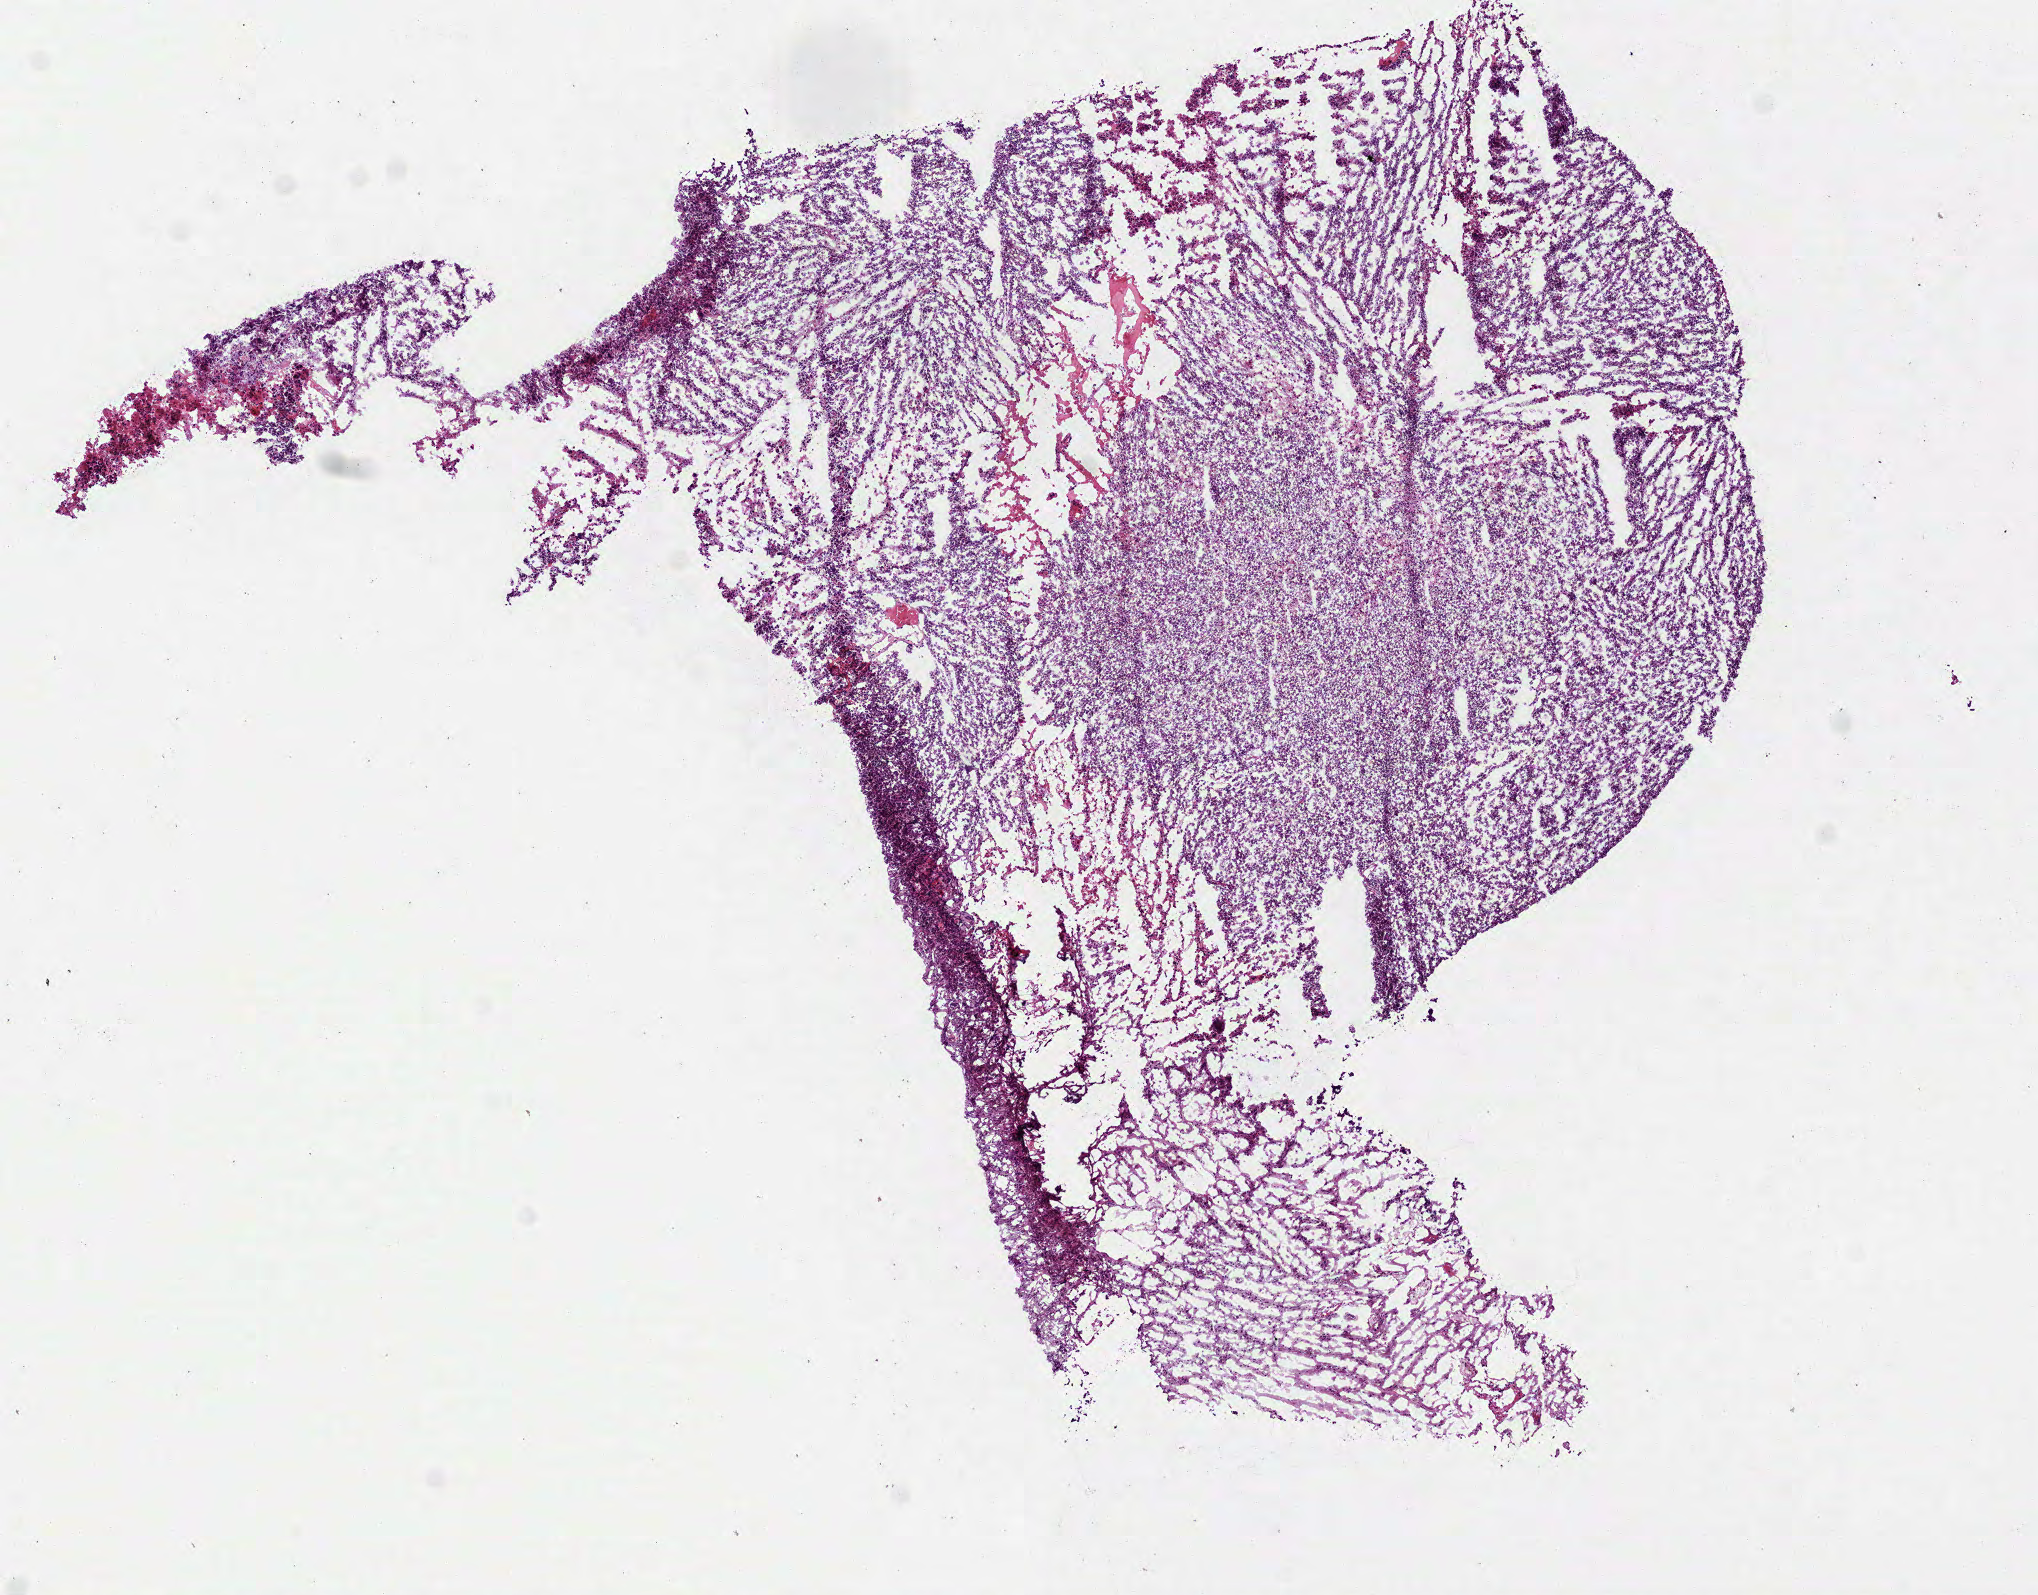
Whole-slide histology image, H&E, shown as a low-resolution overview of the whole scanned area (about 8.2 x 6.4 mm, acquisition: 40x scan), frozen section from the bottom of the tissue portion, sample: primary tumour, brain. Female, age 71 years at initial diagnosis. Slide review estimates, as recorded: tumour cells 85%, tumour nuclei 85%, normal cells 0%, stromal cells 0%, necrosis 15%.
* diagnosis: Glioblastoma